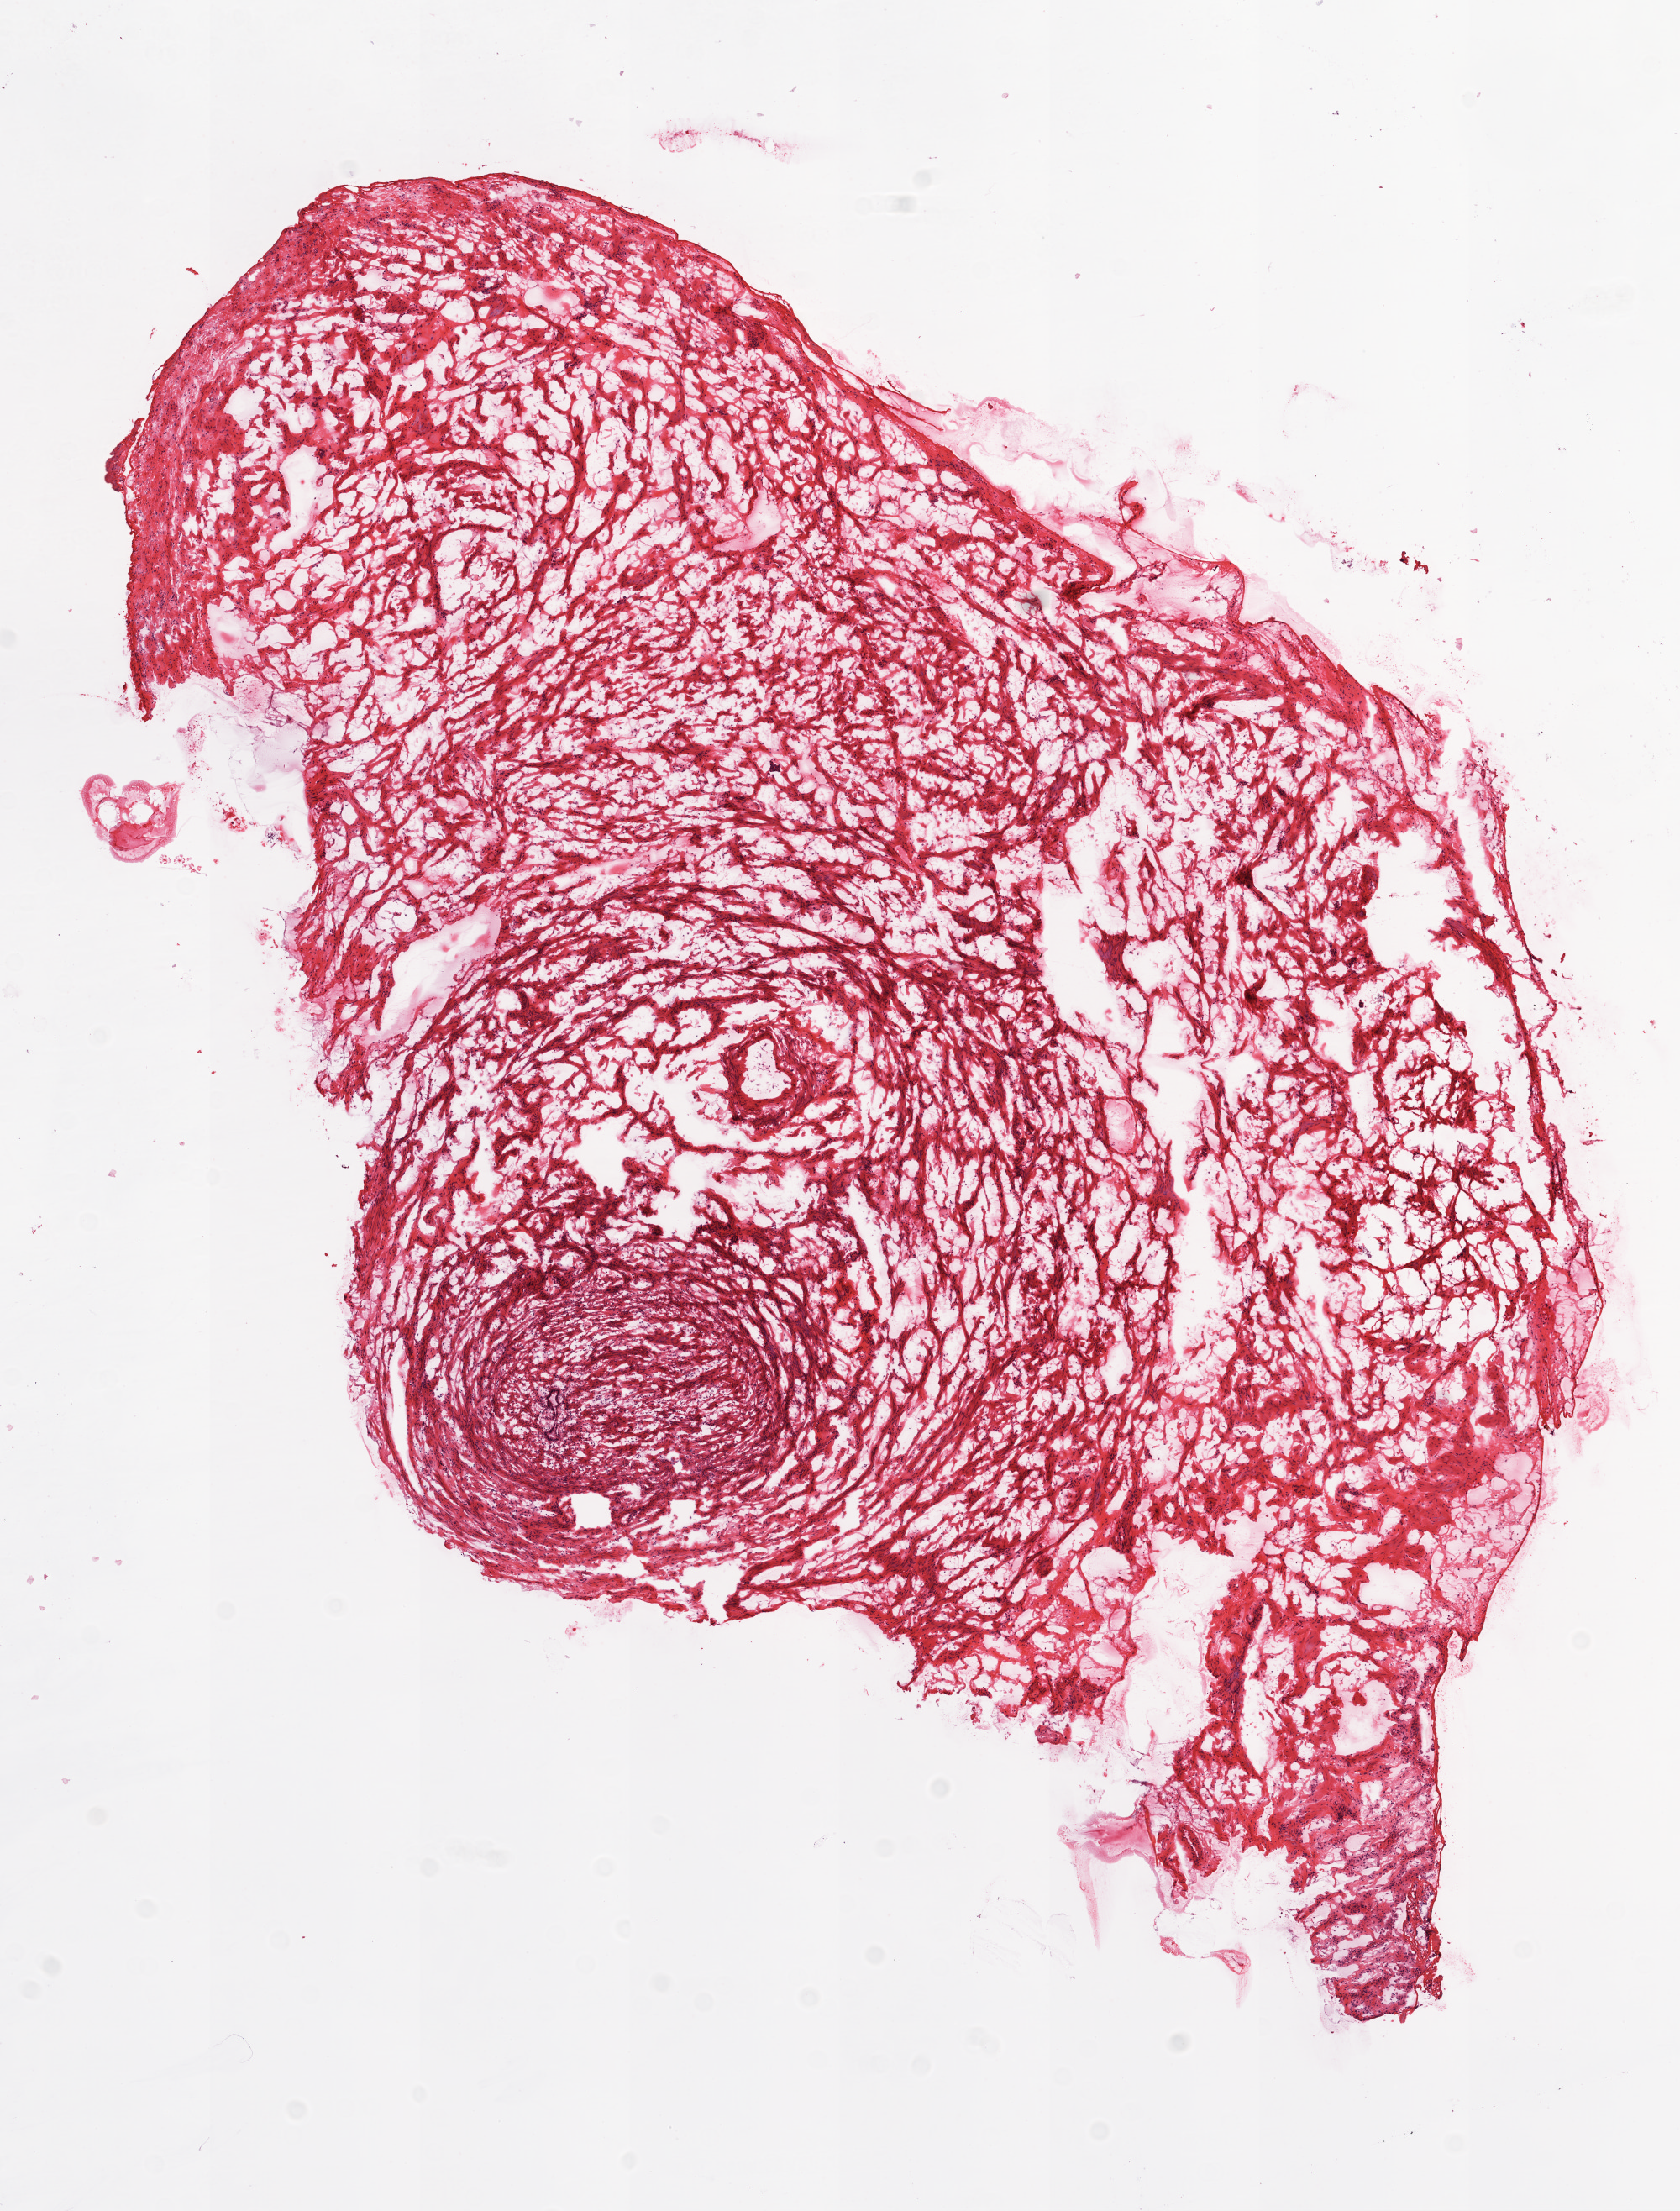
Whole-slide histology image, H&E, a low-resolution overview of the entire scanned area, about 8.0 x 10.6 mm (from a 20x scan). Frozen section from the top of the tissue portion. Ovary, solid tissue normal (non-tumour tissue) sample. Patient: female, age at initial diagnosis 71 years.
This section: solid tissue normal sample (biorepository sample class). Patient diagnosis: Serous cystadenocarcinoma, NOS.